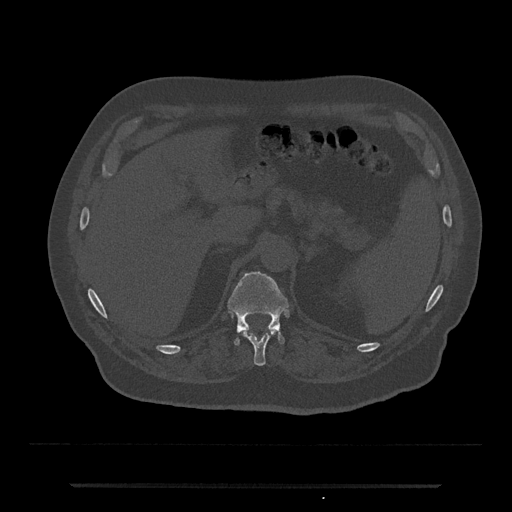
CT including the spine, one axial slice. Position 617 of 797 along the scan axis. Bone window (W 1800 / L 400 HU). 0.5 mm slice thickness. 512 × 512 image matrix, field of view 434 × 434 mm. Male patient, age 80 years. Case-level facts recorded for this patient, not image findings: primary cancer: prostate.
Outlined on this slice (semi-automatically segmented with operator editing):
- T11 vertebra: bounding box <243,330,276,366> (left, top, right, bottom; pixels)
- T12 vertebra: <228,271,289,346>